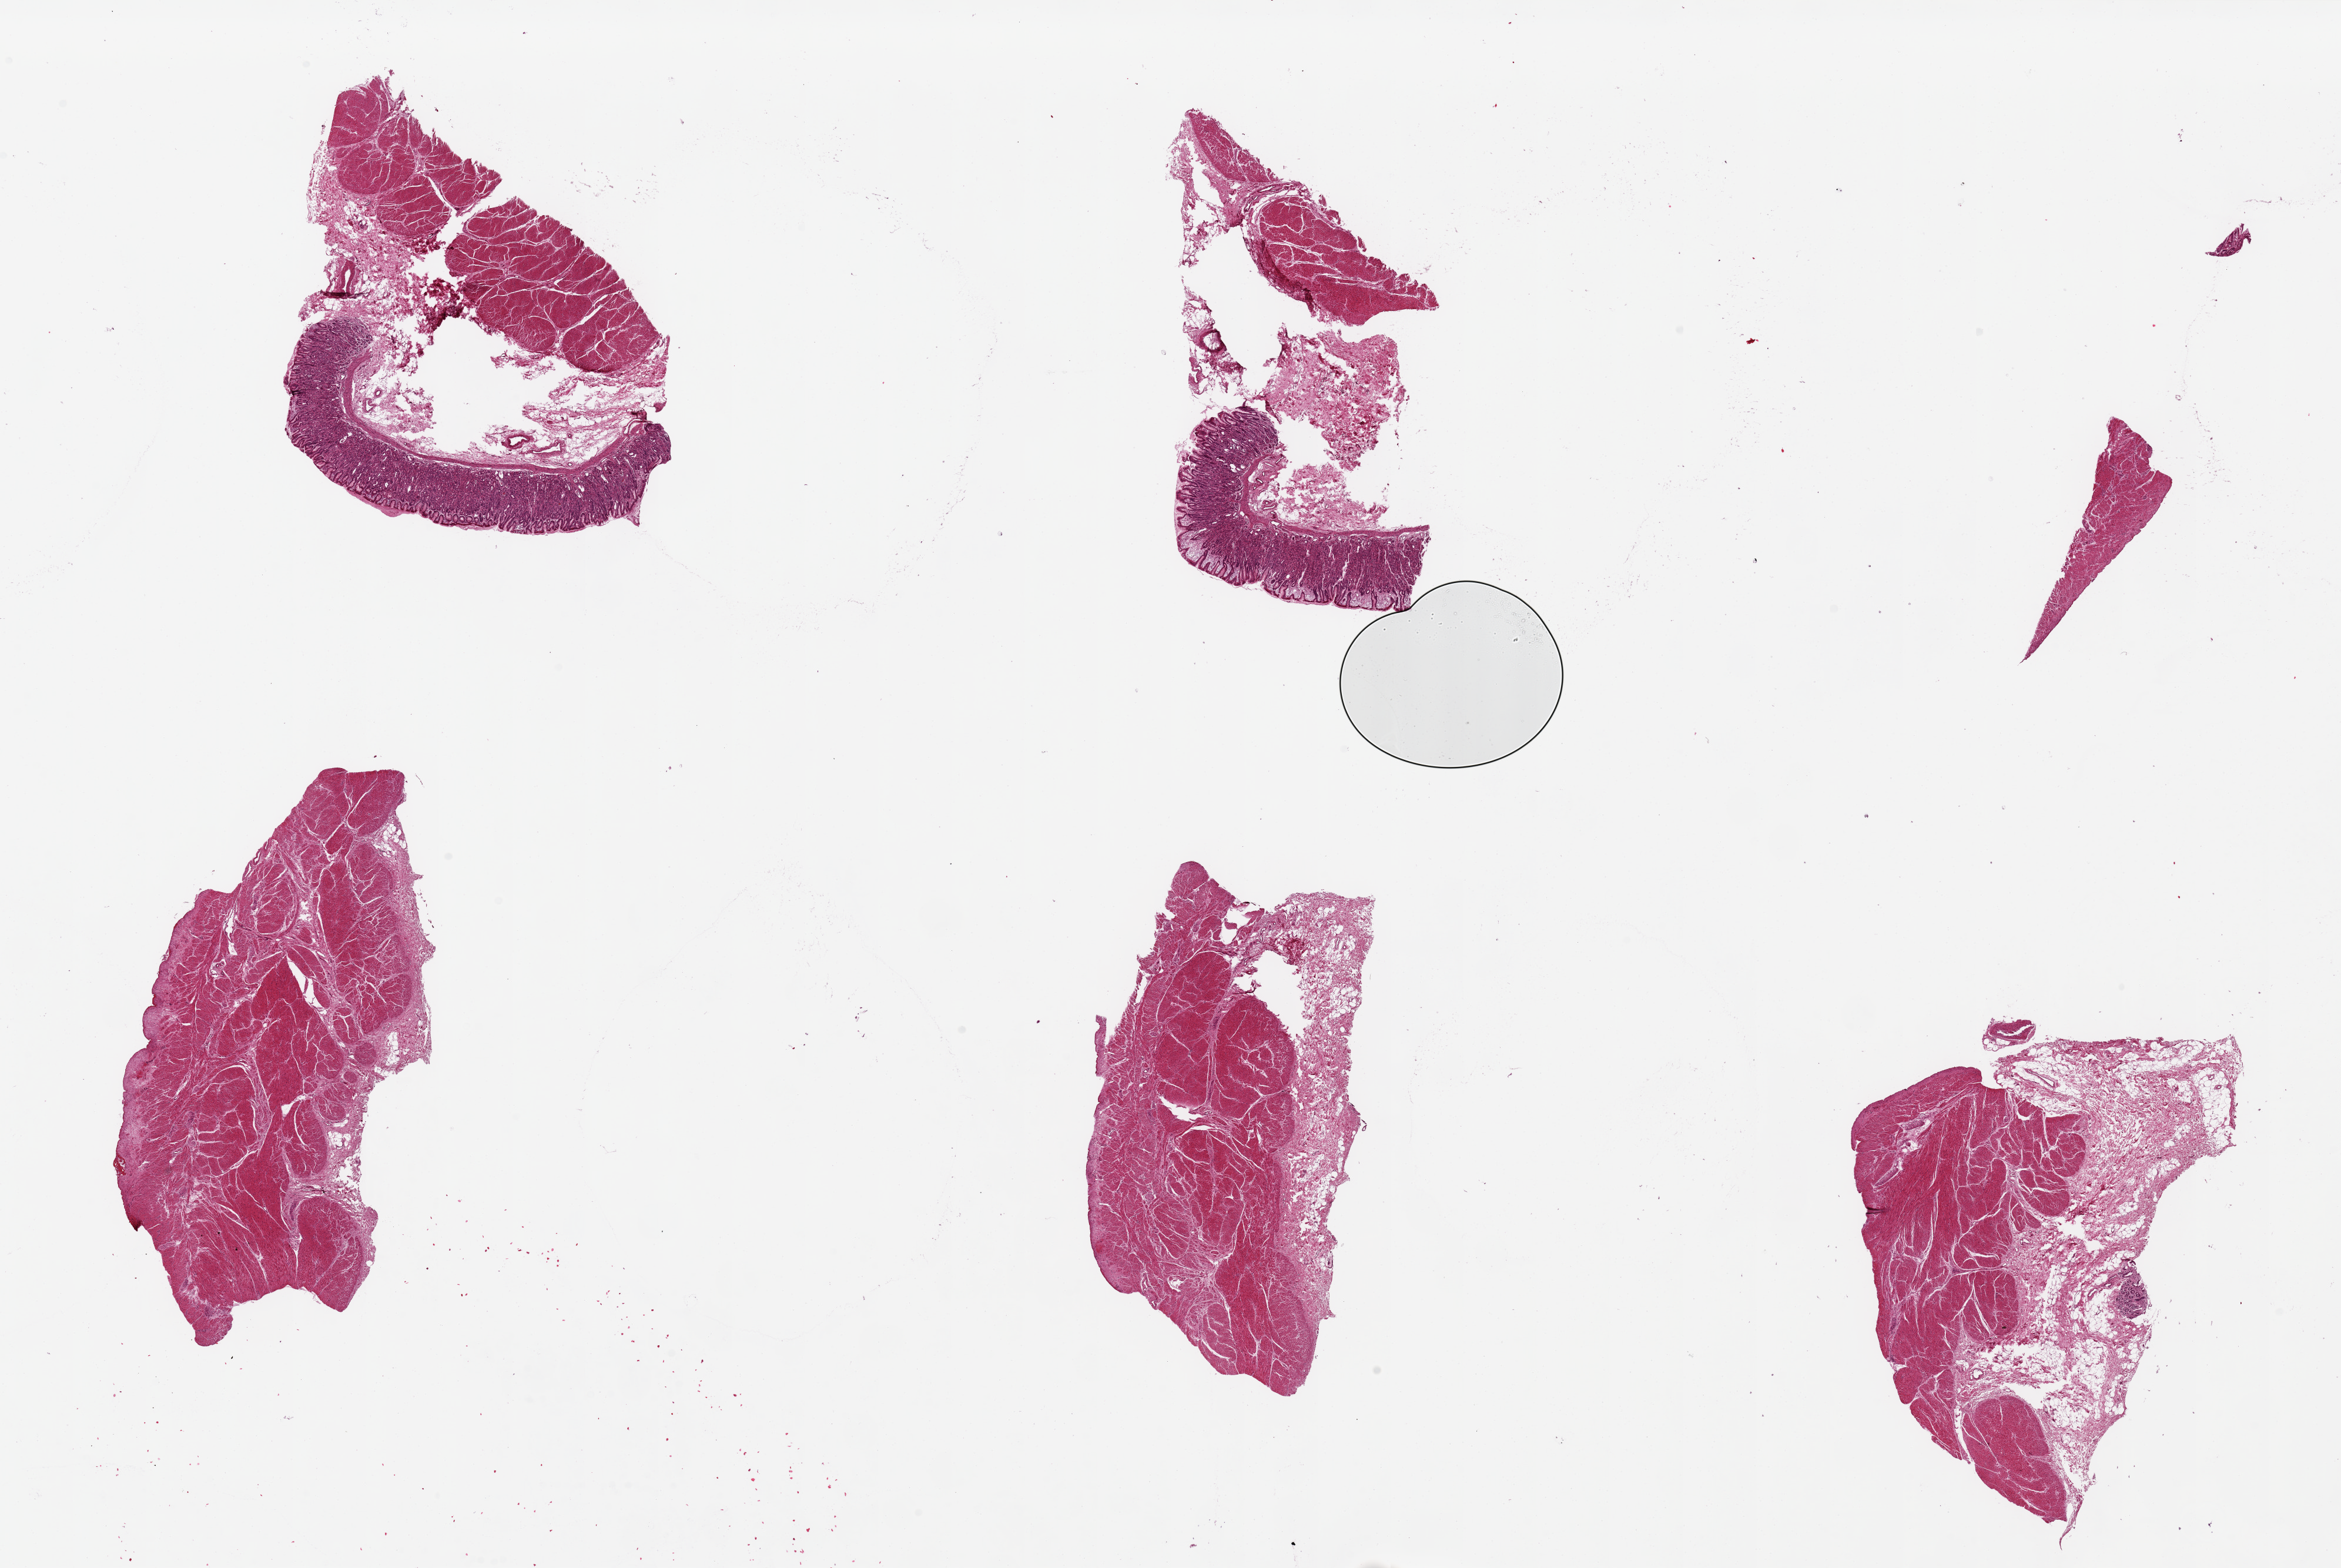
Whole-slide image, haematoxylin and eosin stain — shown as a low-resolution overview of the whole scanned area (about 31.5 x 21.1 mm, acquisition: 20x scan), PAXgene-fixed, paraffin-embedded tissue, target tissue: stomach, tissue donor sample.
- reviewer comment on this tissue sample: 6 pieces, up to 8x4mm; only 2 with mucosa, 4 with muscularis propria only